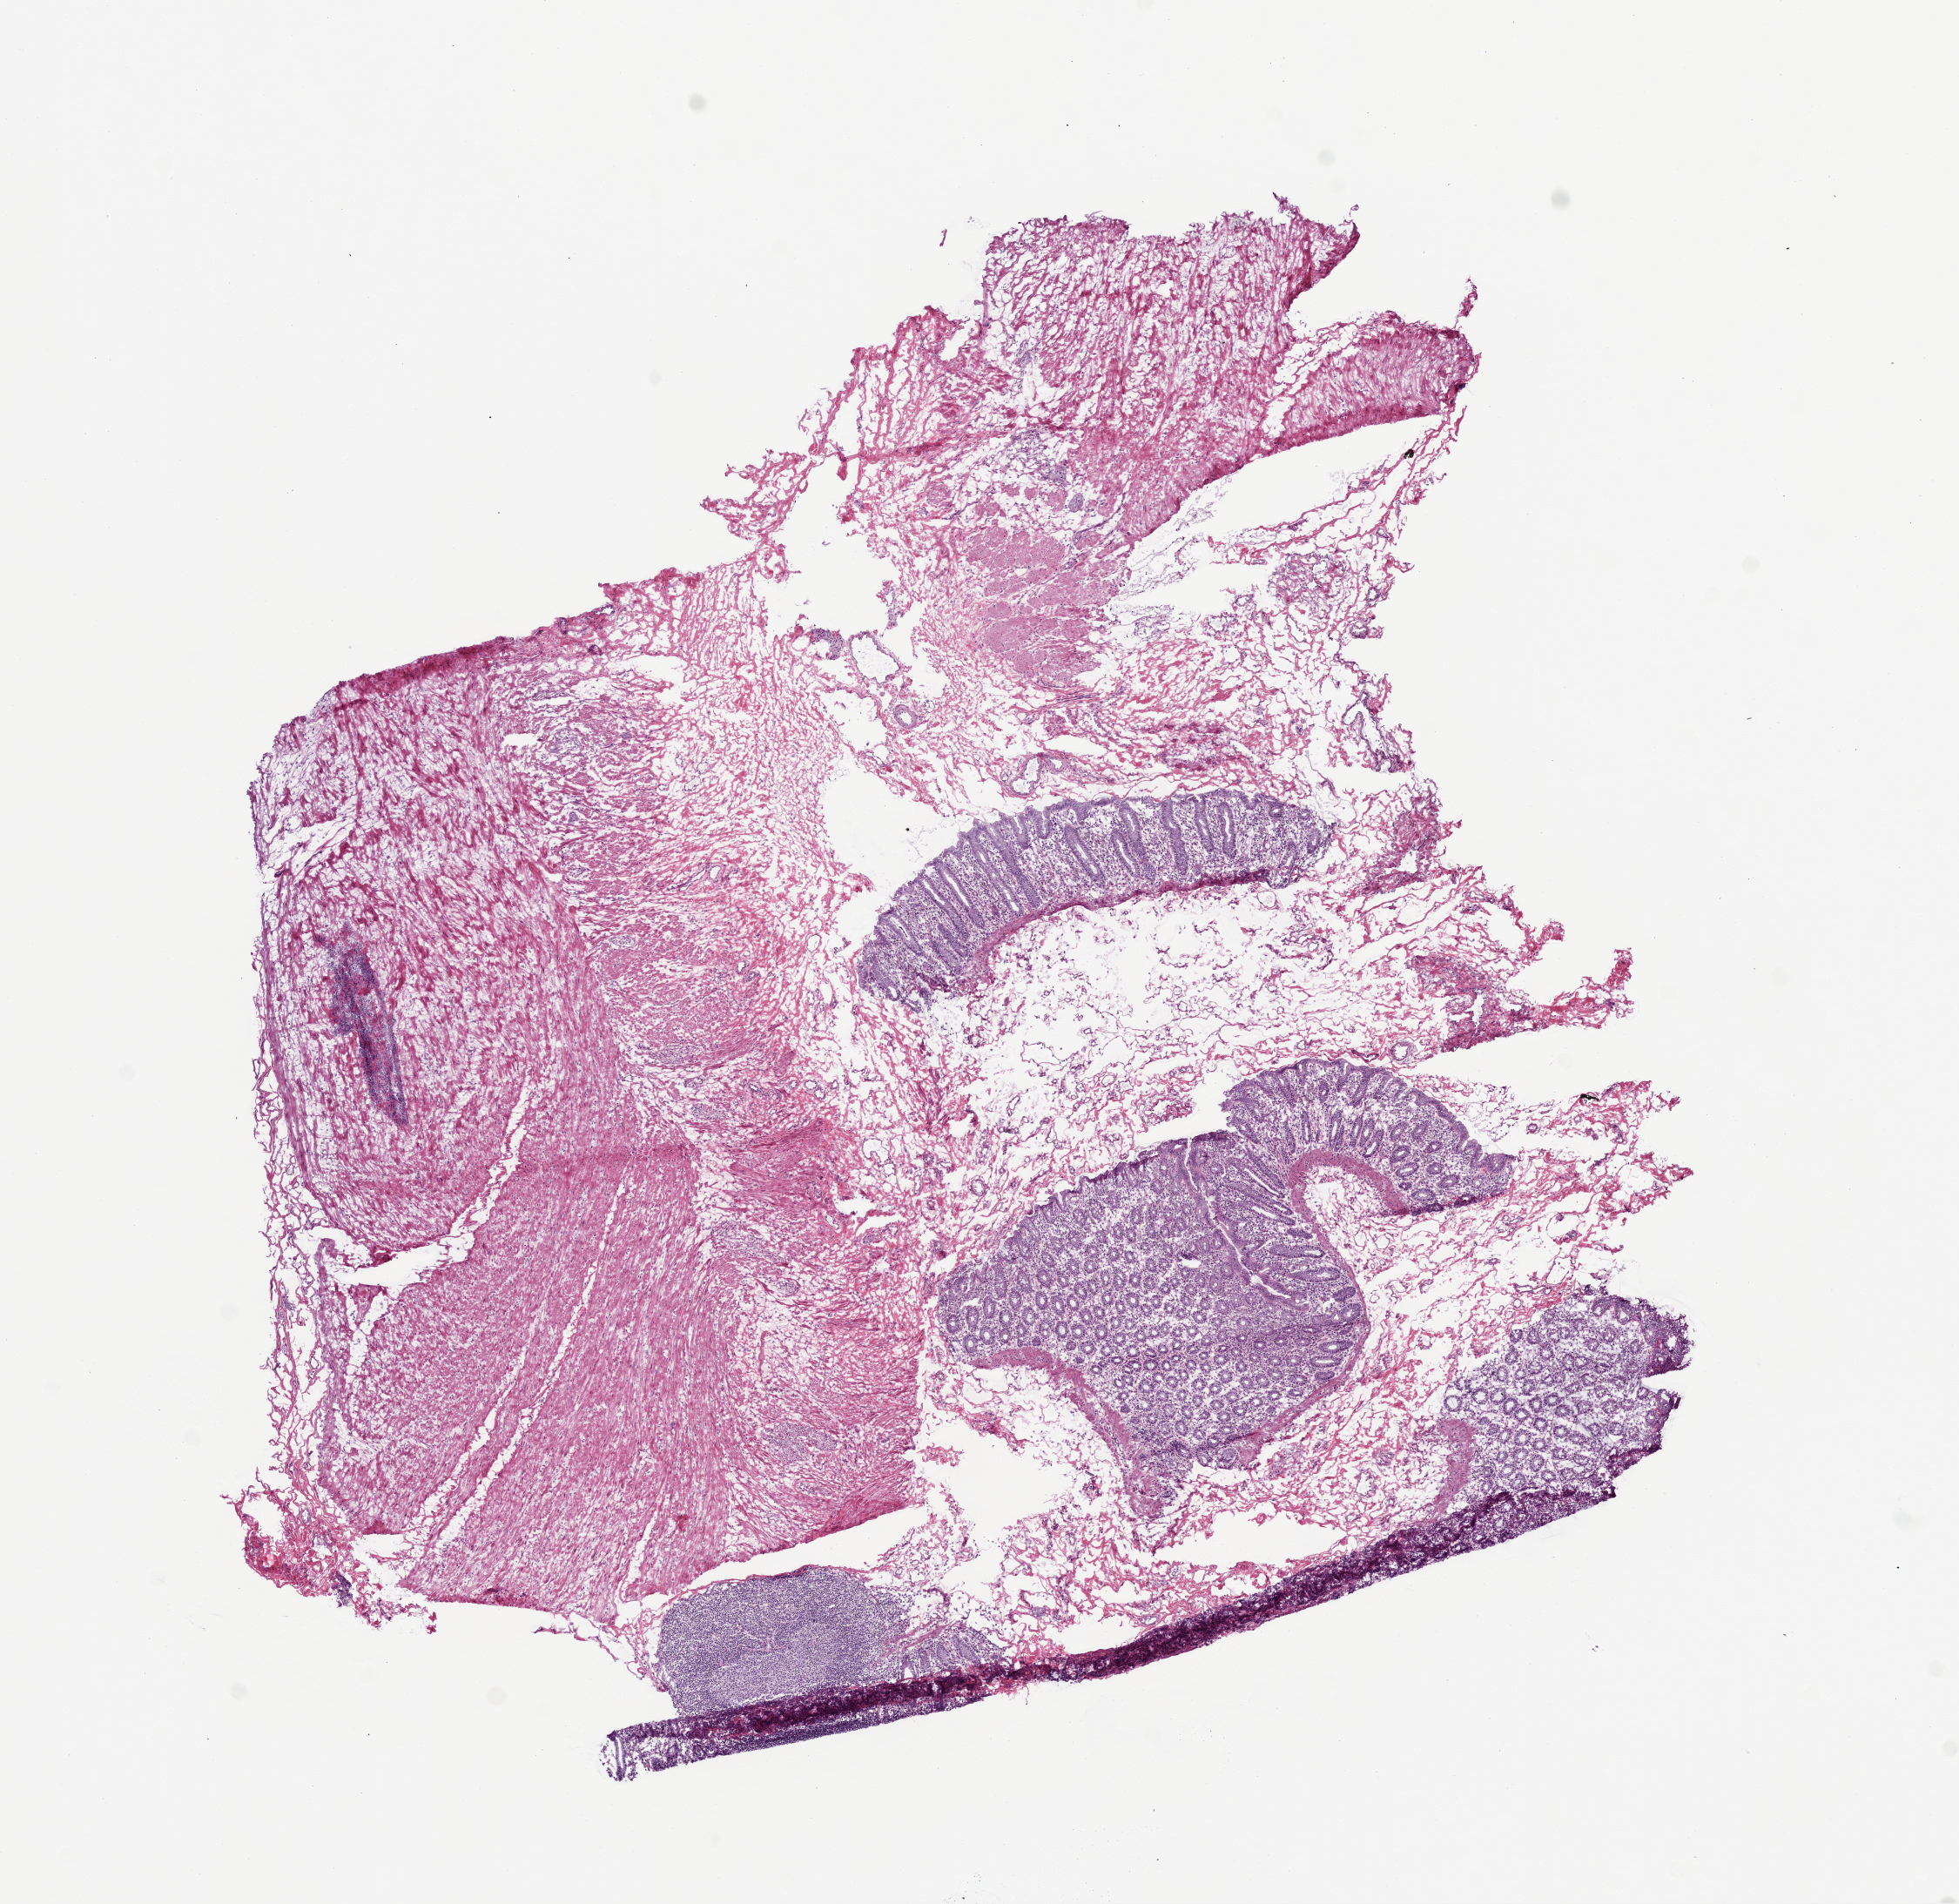
H&E whole-slide image, shown as a low-resolution overview of the whole scanned area (about 9.0 x 8.8 mm, acquisition: 20x scan), frozen section, solid tissue normal (non-tumour tissue) sample from the colon. Patient: male, age at initial diagnosis 77 years.
This section: solid tissue normal sample (biorepository sample class). Patient diagnosis: Adenocarcinoma, NOS.